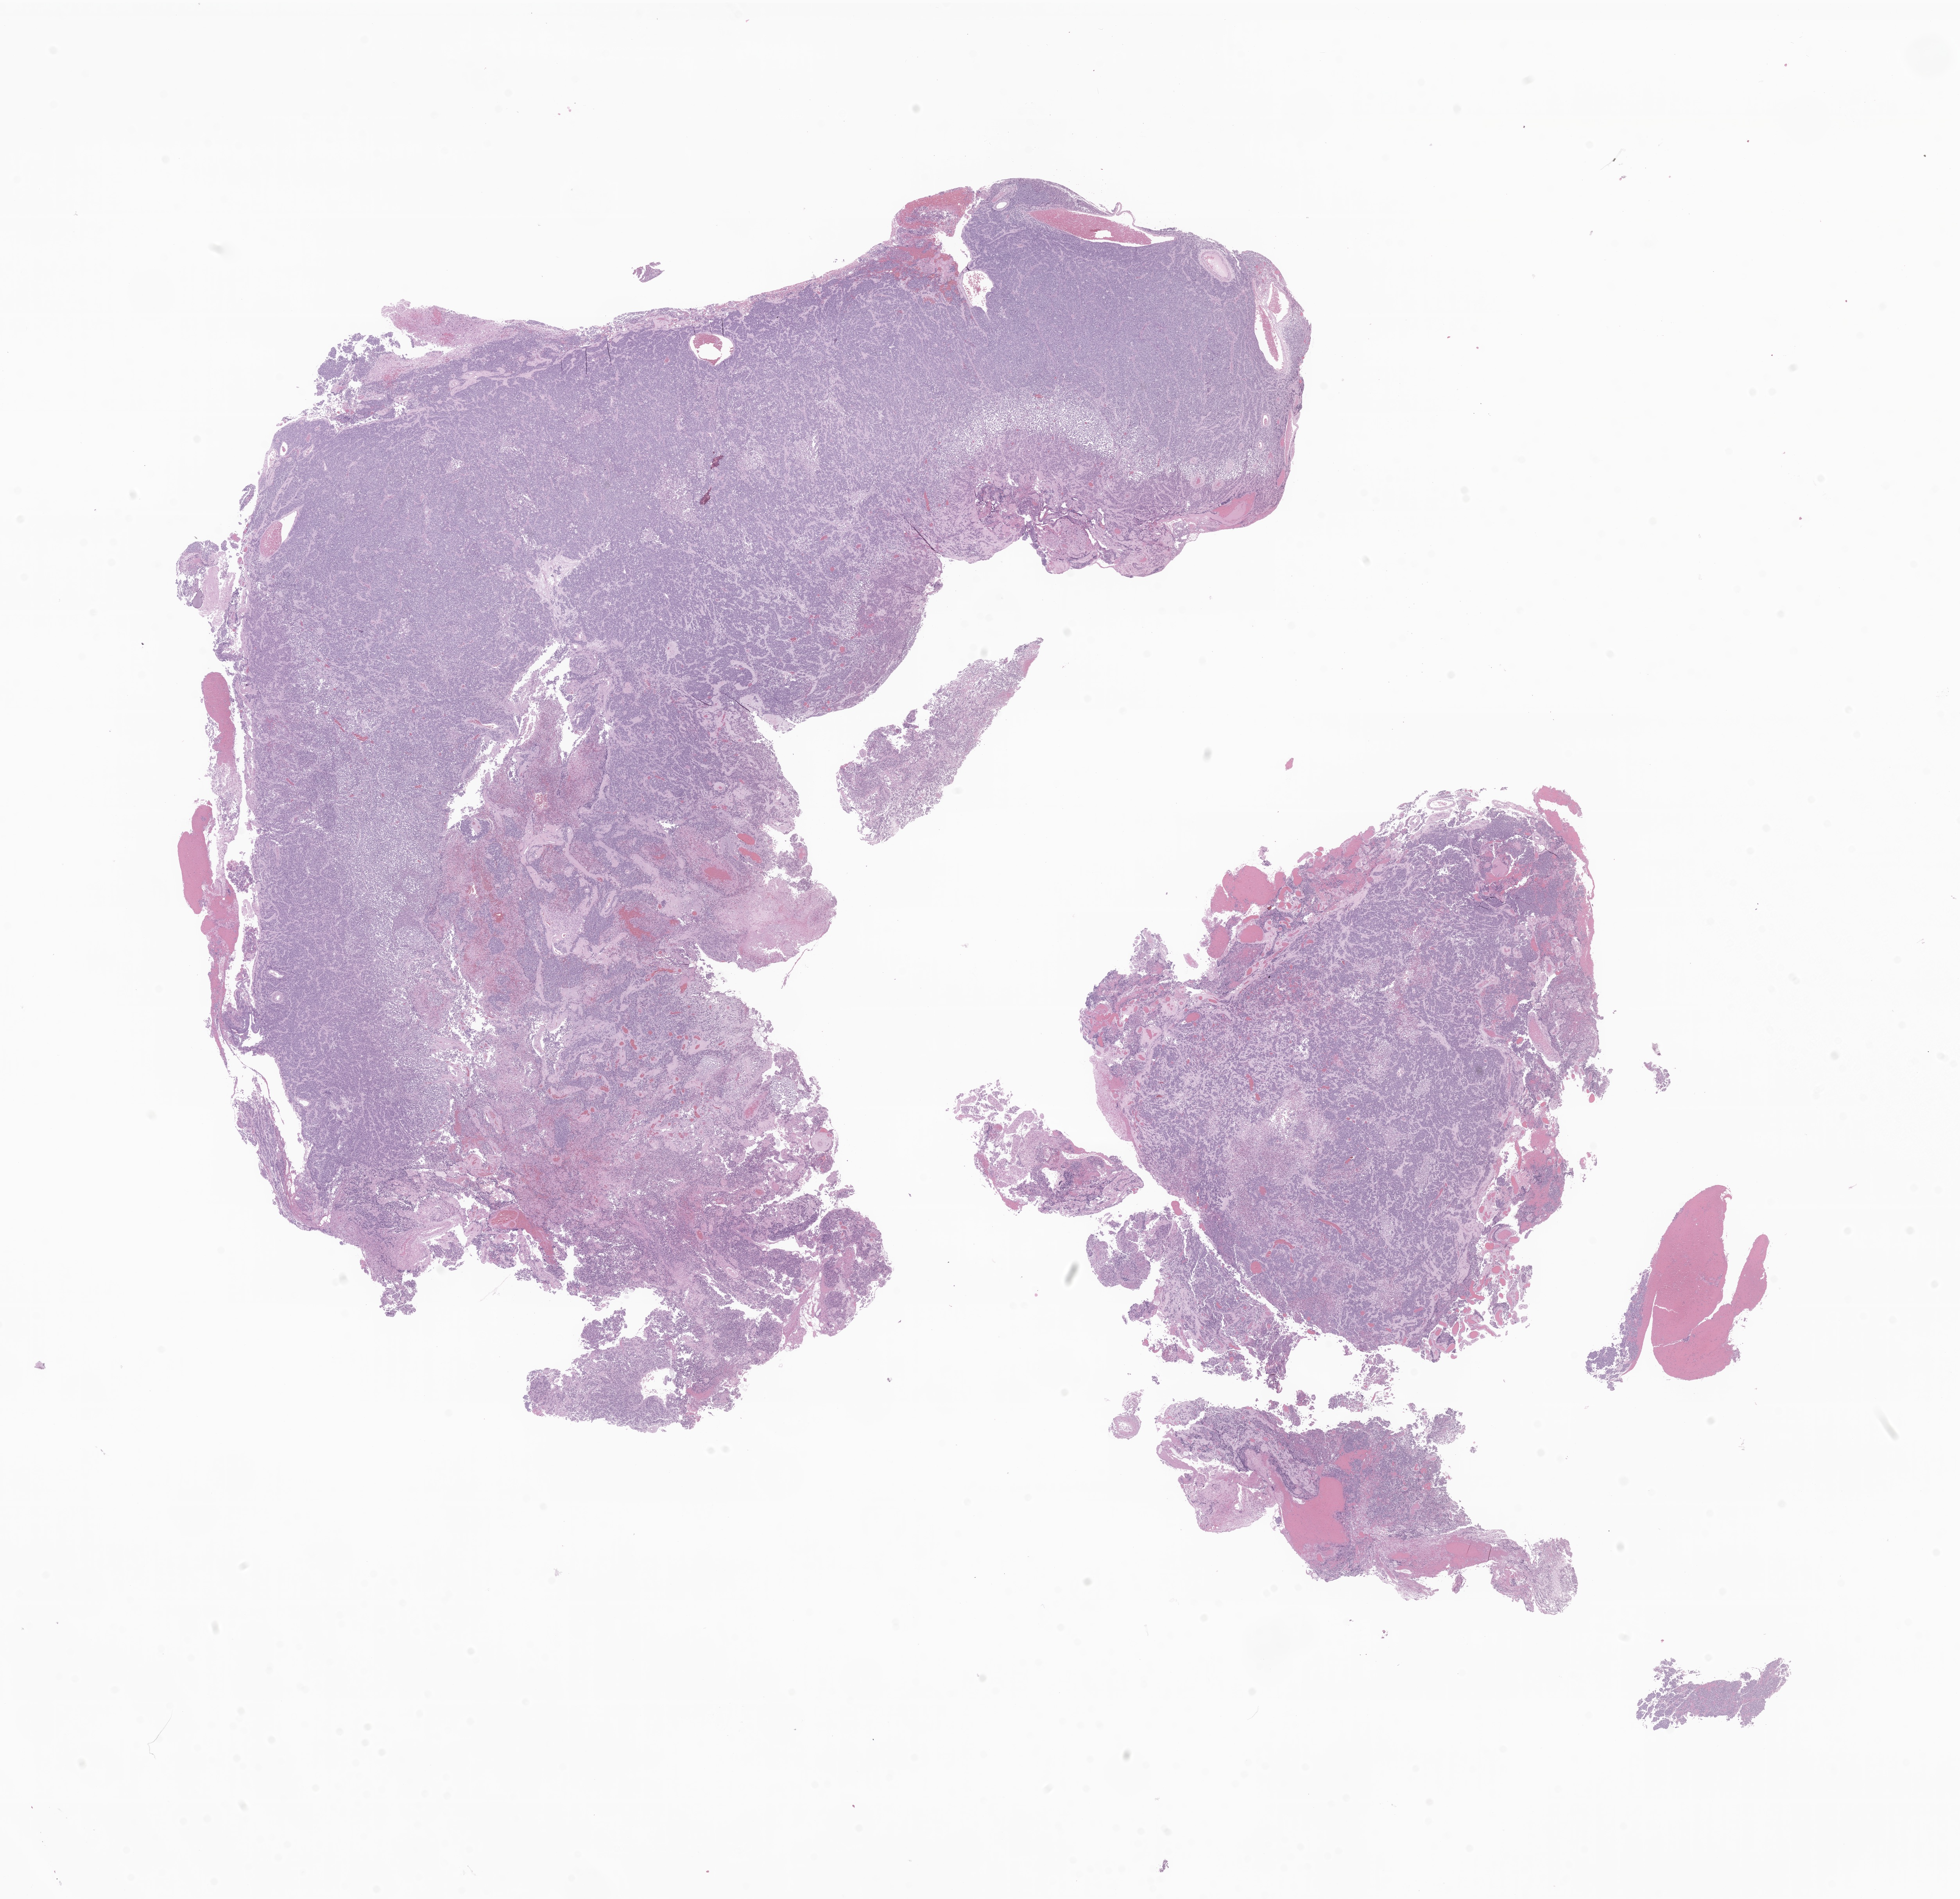
H&E whole-slide image of tumor tissue from the brain — shown as a low-resolution overview of the whole scanned area (about 21.1 x 20.5 mm). Formalin-fixed, paraffin-embedded (FFPE) tissue. Patient female; age 88 months (7 years 4 months).
Diagnosis: Medulloblastoma, NOS.